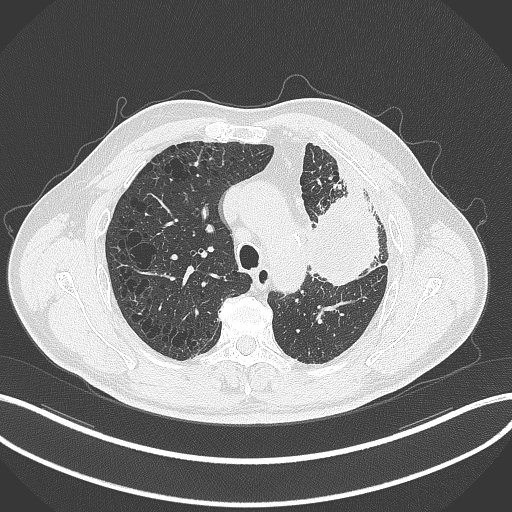
Chest CT, one axial slice; slice 224 of 297 in the series (ordered by position); reconstruction kernel B70f; 120 kVp; lung window (W 1500 / L -600 HU); 1 mm slice thickness; 512 × 512 image matrix. Patient: male, 68 years. From the clinical record (not read from this slice): clinical TNM (as recorded): T3 N3 M1.
Outlined on this slice (bounding box drawn by a radiologist):
- lung tumour (recorded histology: adenocarcinoma): bounding box [x1, y1, x2, y2] px = [303, 181, 390, 289]